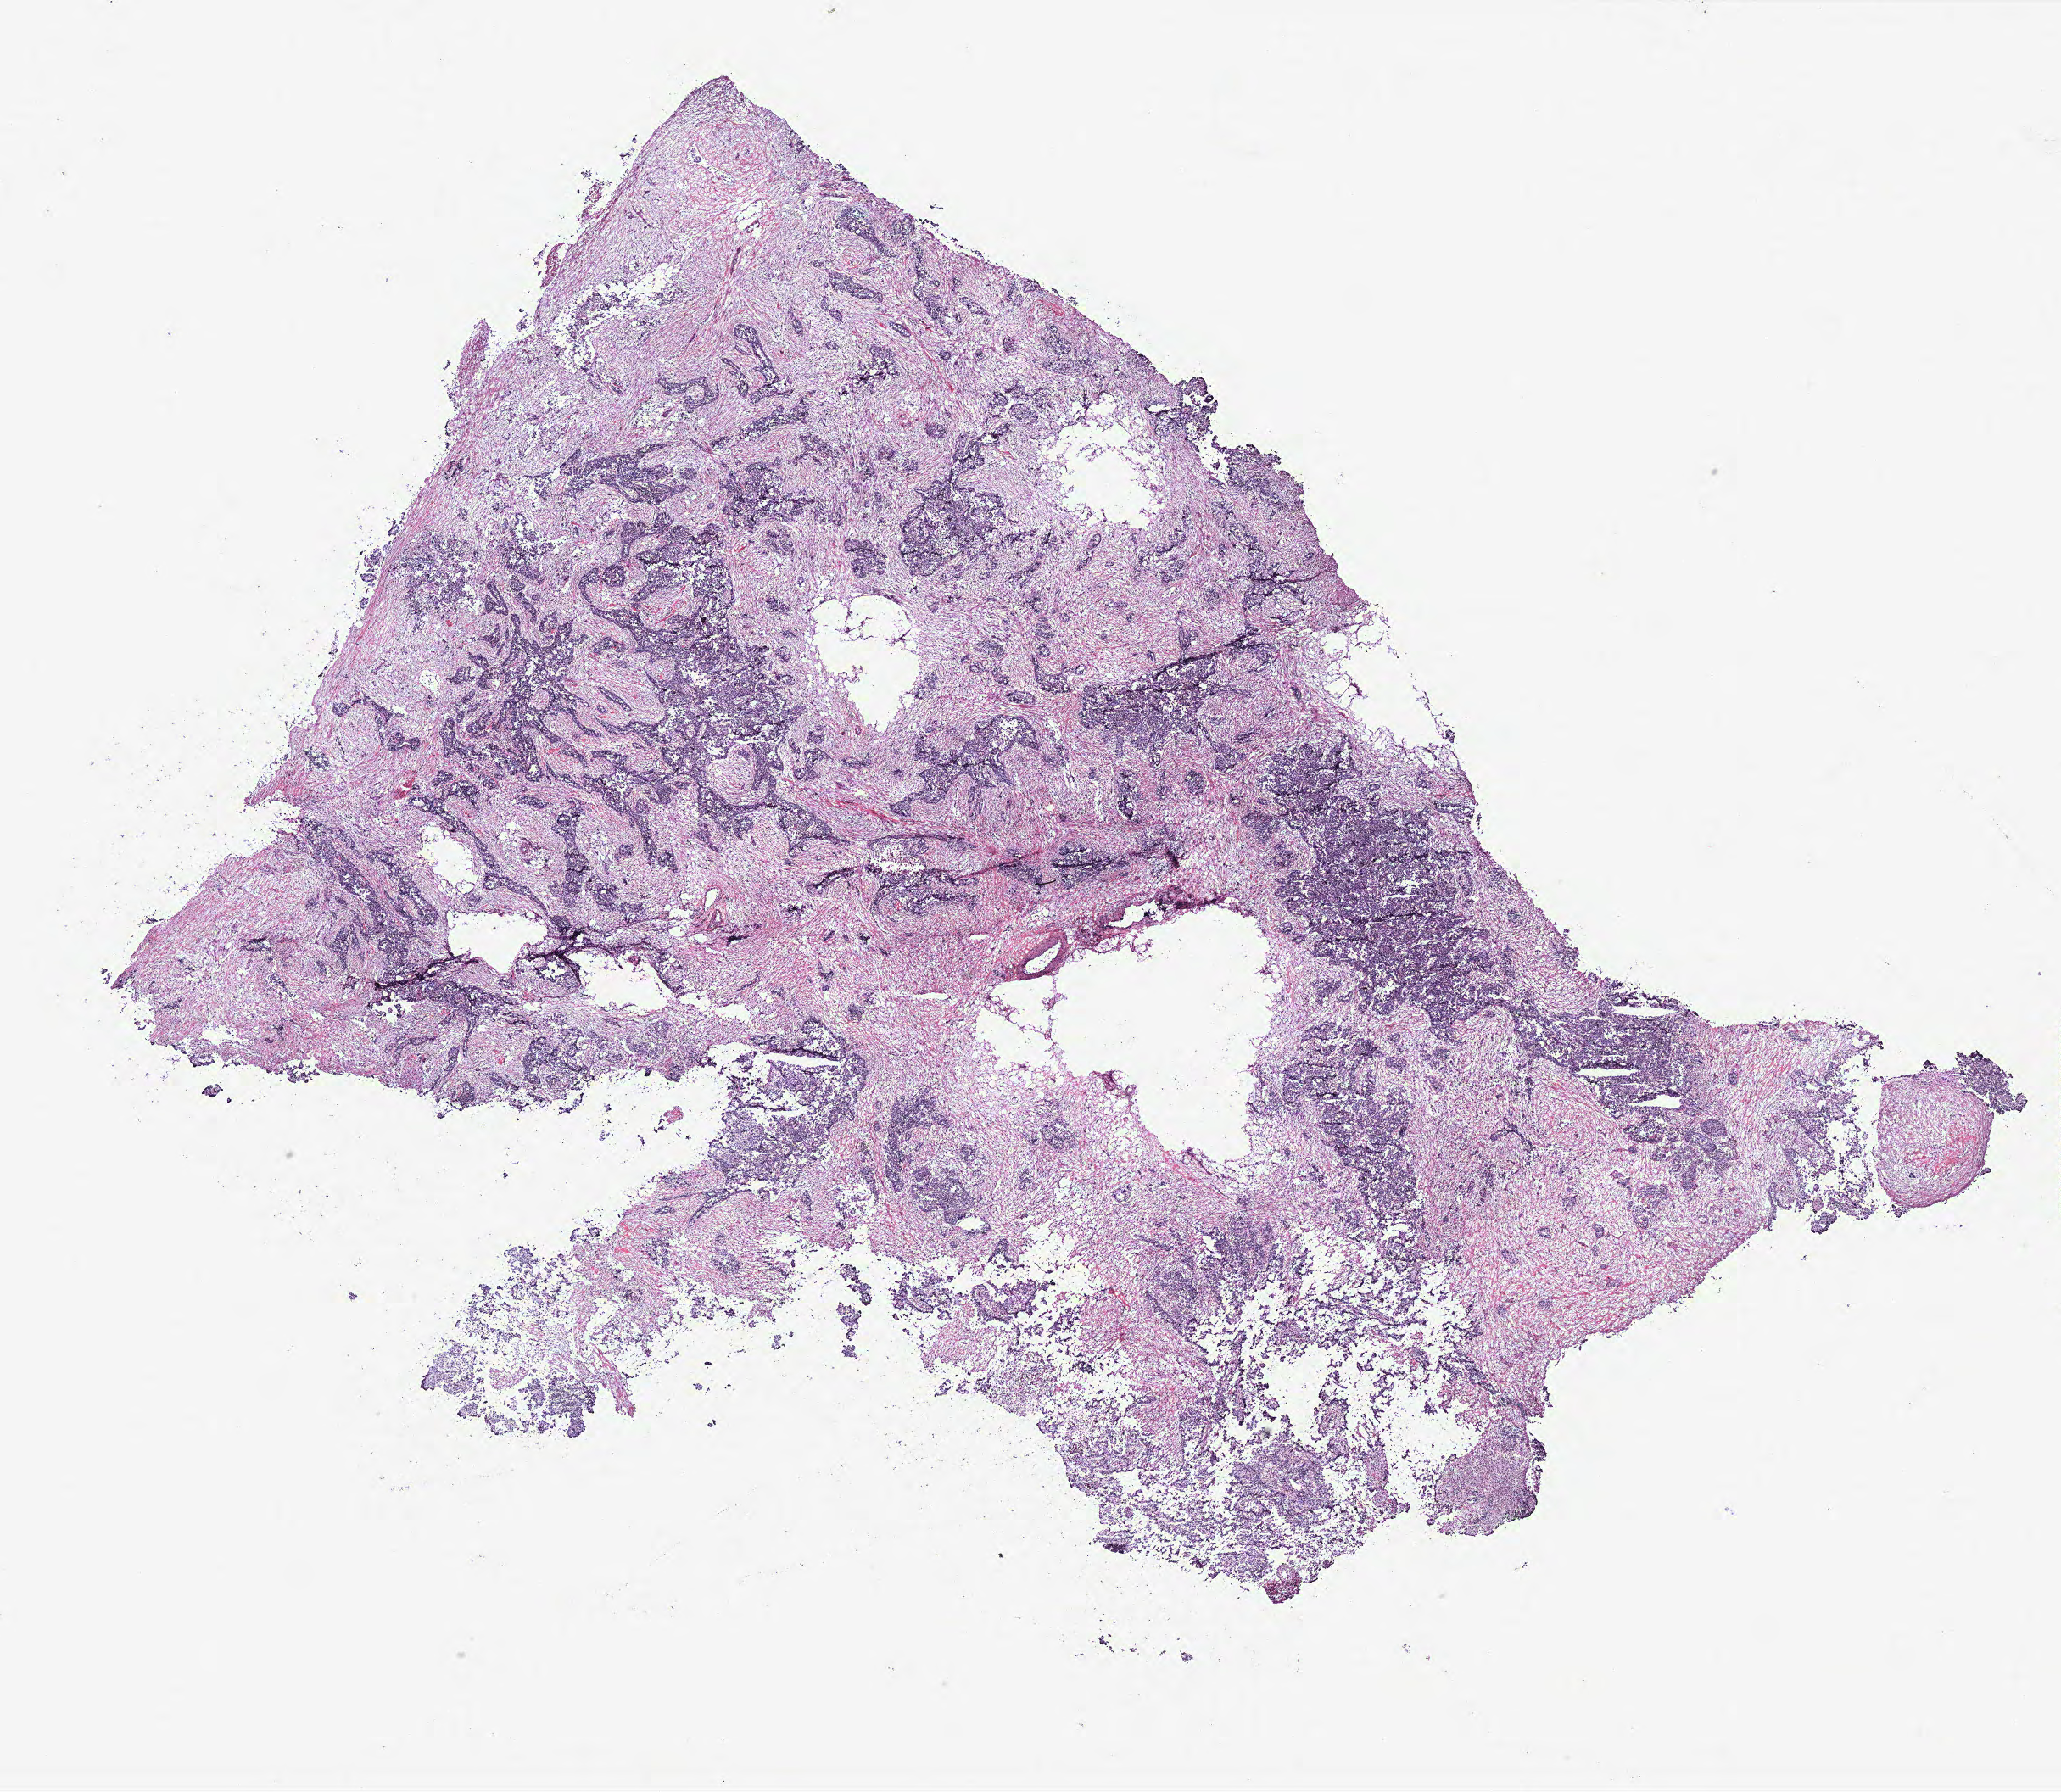
Whole-slide histology image, Hematoxylin and eosin (H&E) stained — low-resolution overview of the scanned area, about 19.4 x 16.9 mm. Tumour tissue sample, ovary. Patient: female, age 59 years.
Diagnosis: Serous adenocarcinoma, NOS (fallopian tube). Primary tumour site (as recorded): fallopian tube.